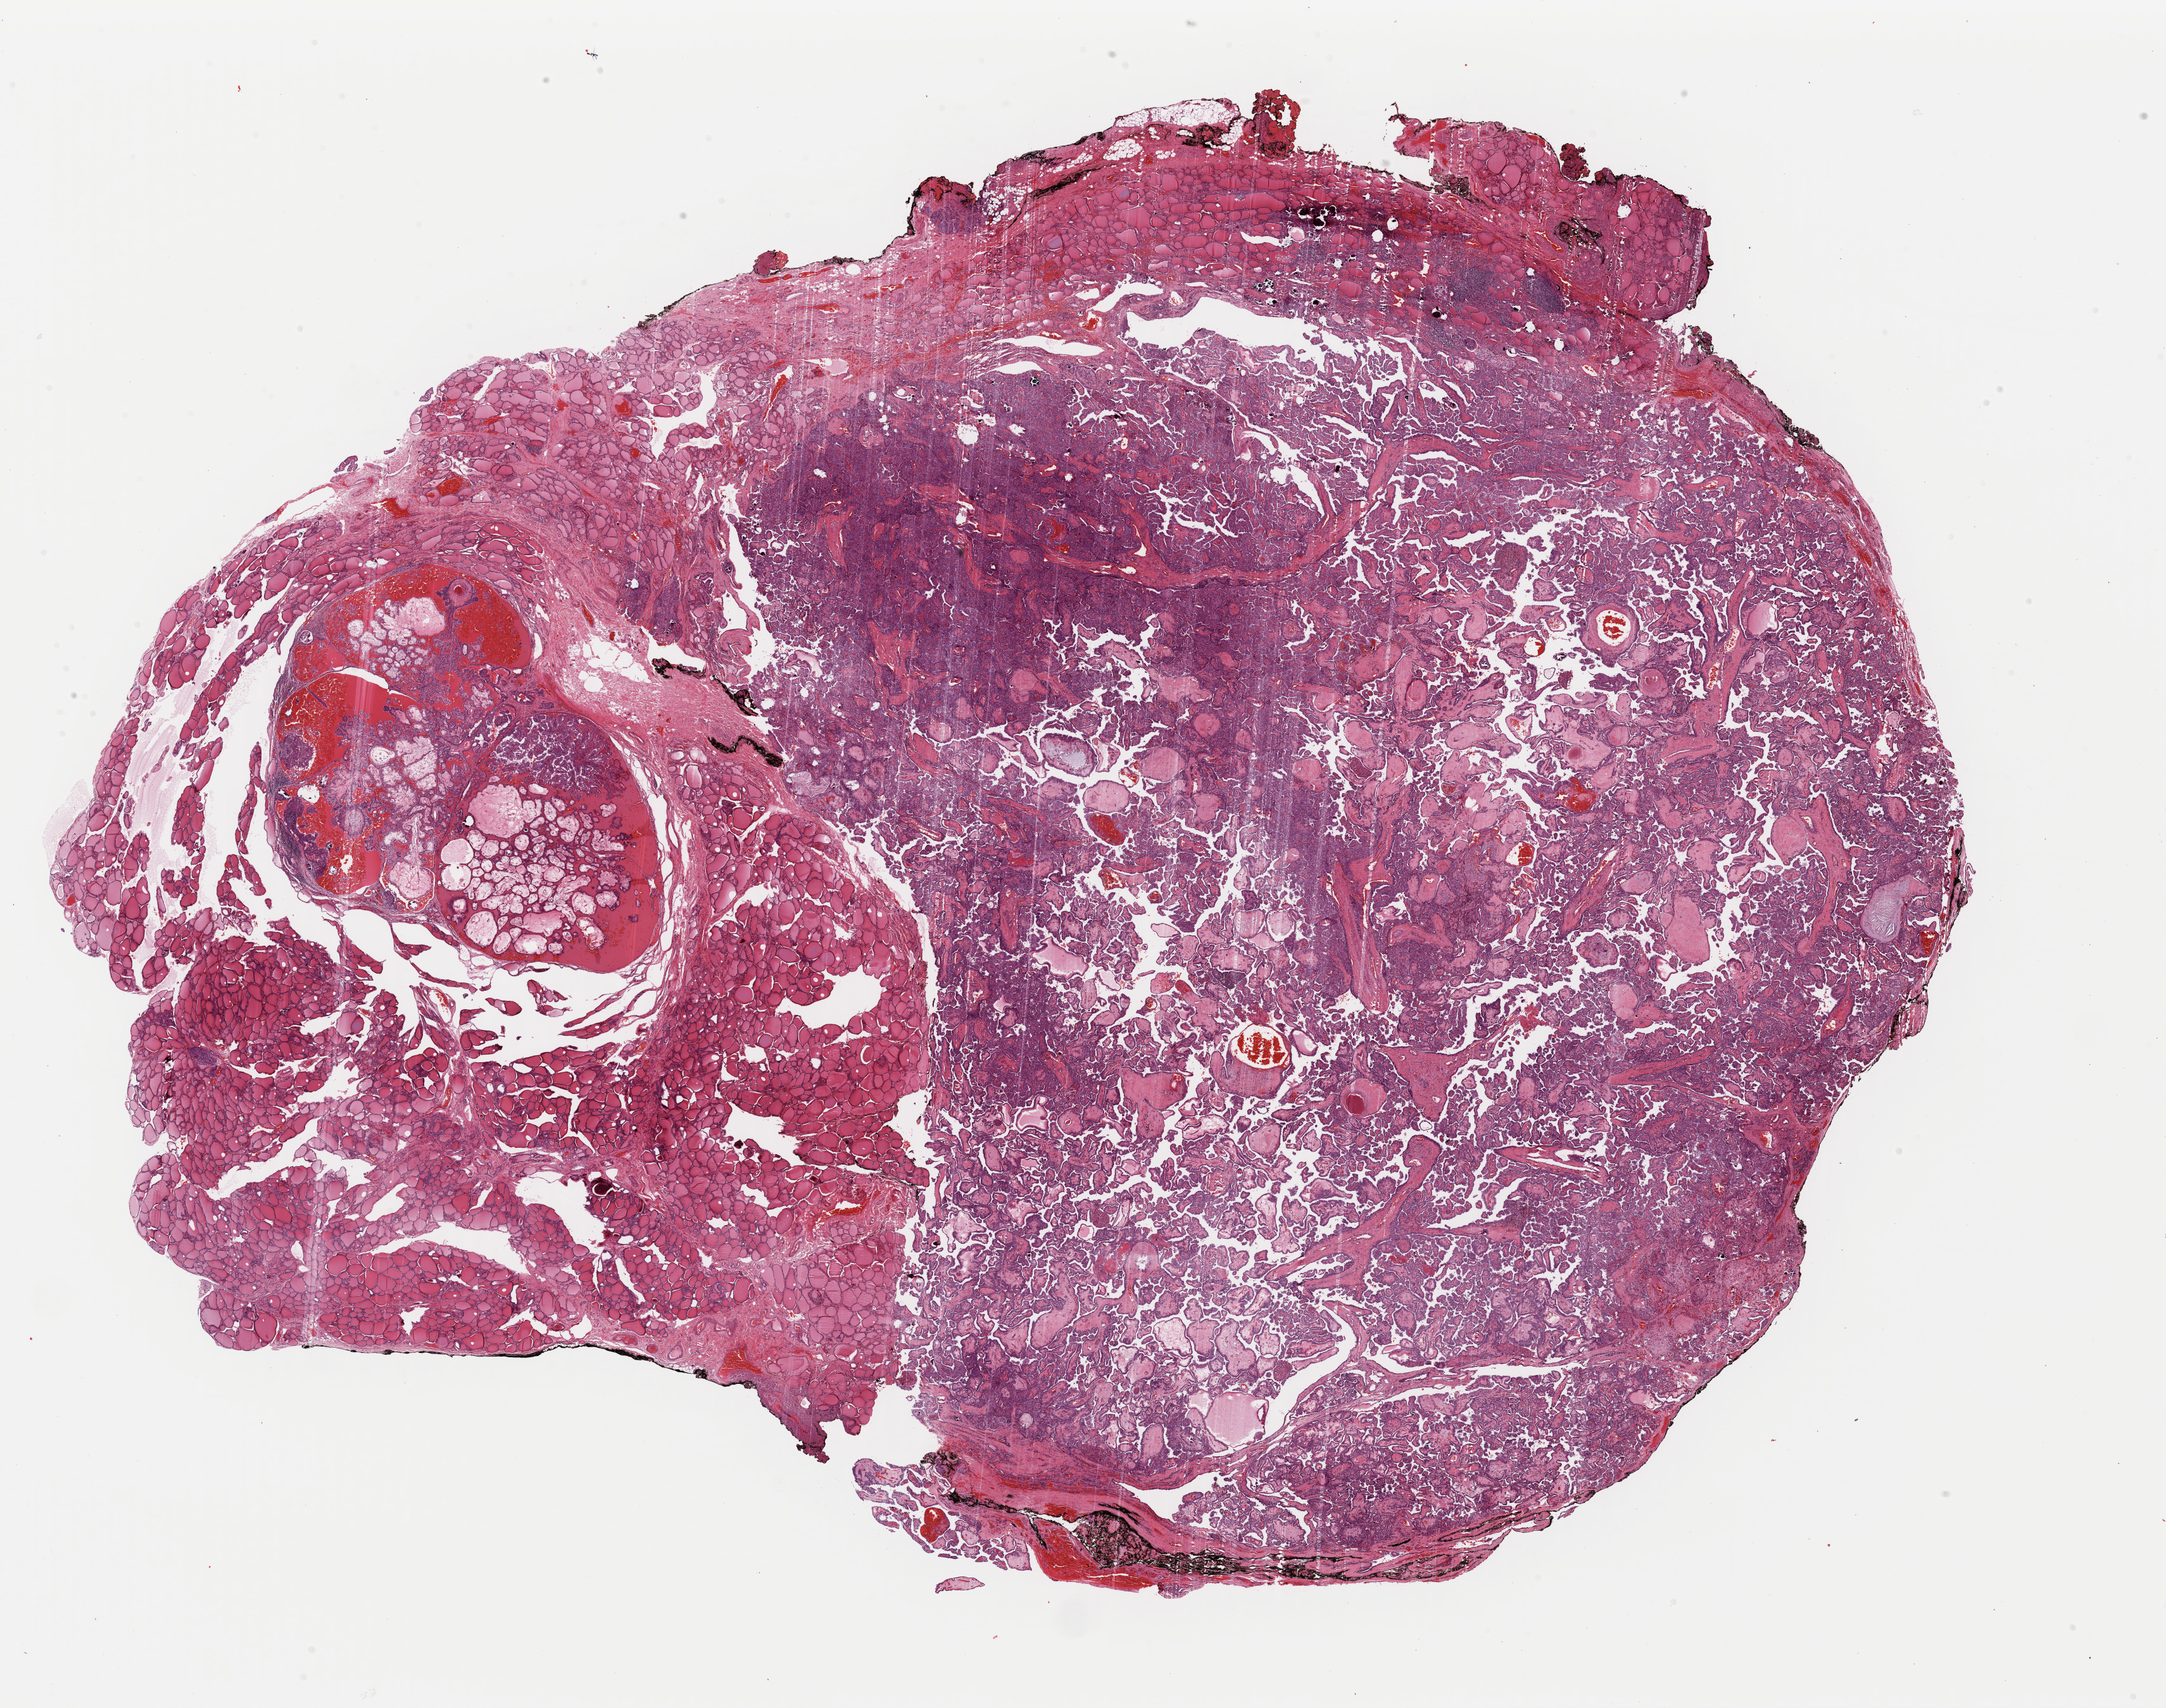
Digitized H&E tissue section (whole slide) — low-resolution overview of the scanned area, about 27.0 x 21.3 mm. Formalin-fixed paraffin-embedded (FFPE) diagnostic section. Sample: primary tumour, thyroid. Female, age 59 years at initial diagnosis.
Diagnosis: Papillary adenocarcinoma, NOS (thyroid gland). Laterality: left. AJCC pathologic stage: III. Lymph nodes positive (case pathology): 7 of 8 examined.